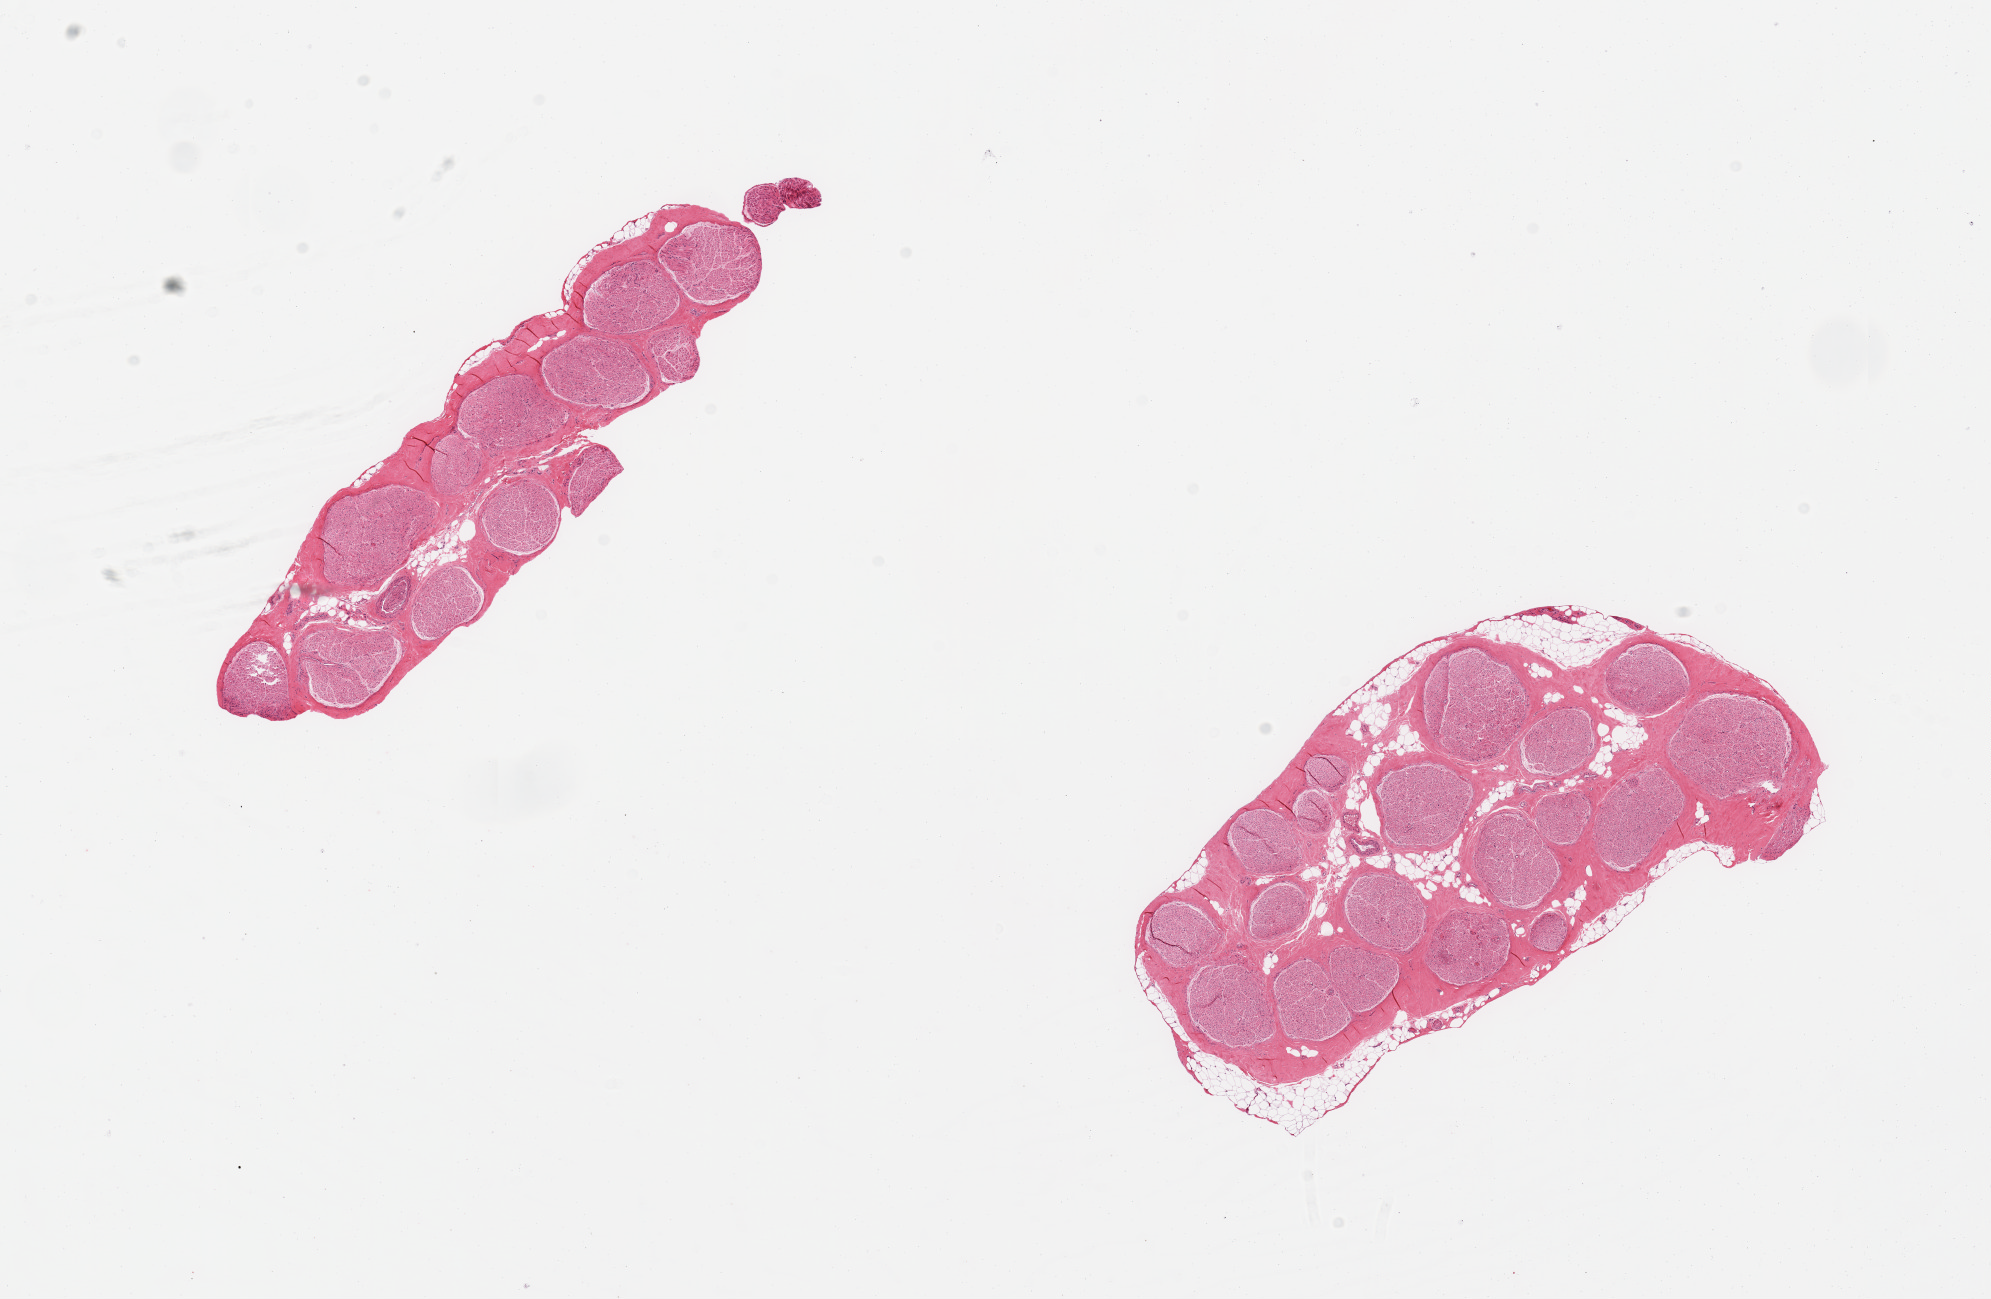
Whole-slide image, H&E stain — shown as a low-resolution overview of the whole scanned area (about 15.8 x 10.3 mm); PAXgene-fixed, paraffin-embedded tissue; sampled site (target tissue): tibial nerve; tissue donor sample. Male donor.
Review note (as recorded): 2 pieces, one includes ~10% fat.